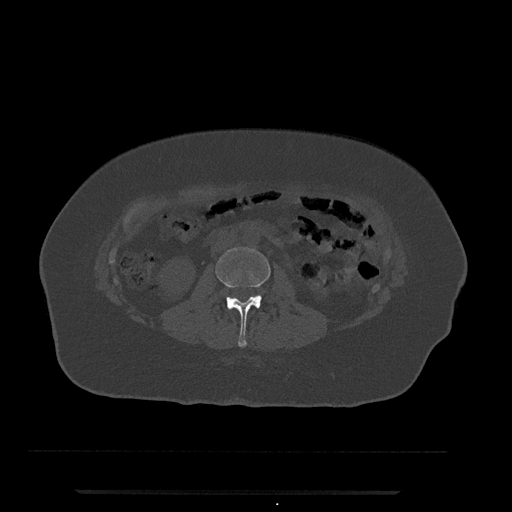
CT including the spine, one axial slice; slice 25 of 797 in the series (ordered by position); bone window (W 1800 / L 400 HU); 512 × 512 image matrix. Female patient, age 51 years. From the clinical record (not read from this slice): primary cancer: neuro; vertebrae with lytic lesions (as recorded): T8.
Structures marked on this image (semi-automatically segmented with operator editing):
- L2 vertebra: bounding box <215,247,270,347> (left, top, right, bottom; pixels)